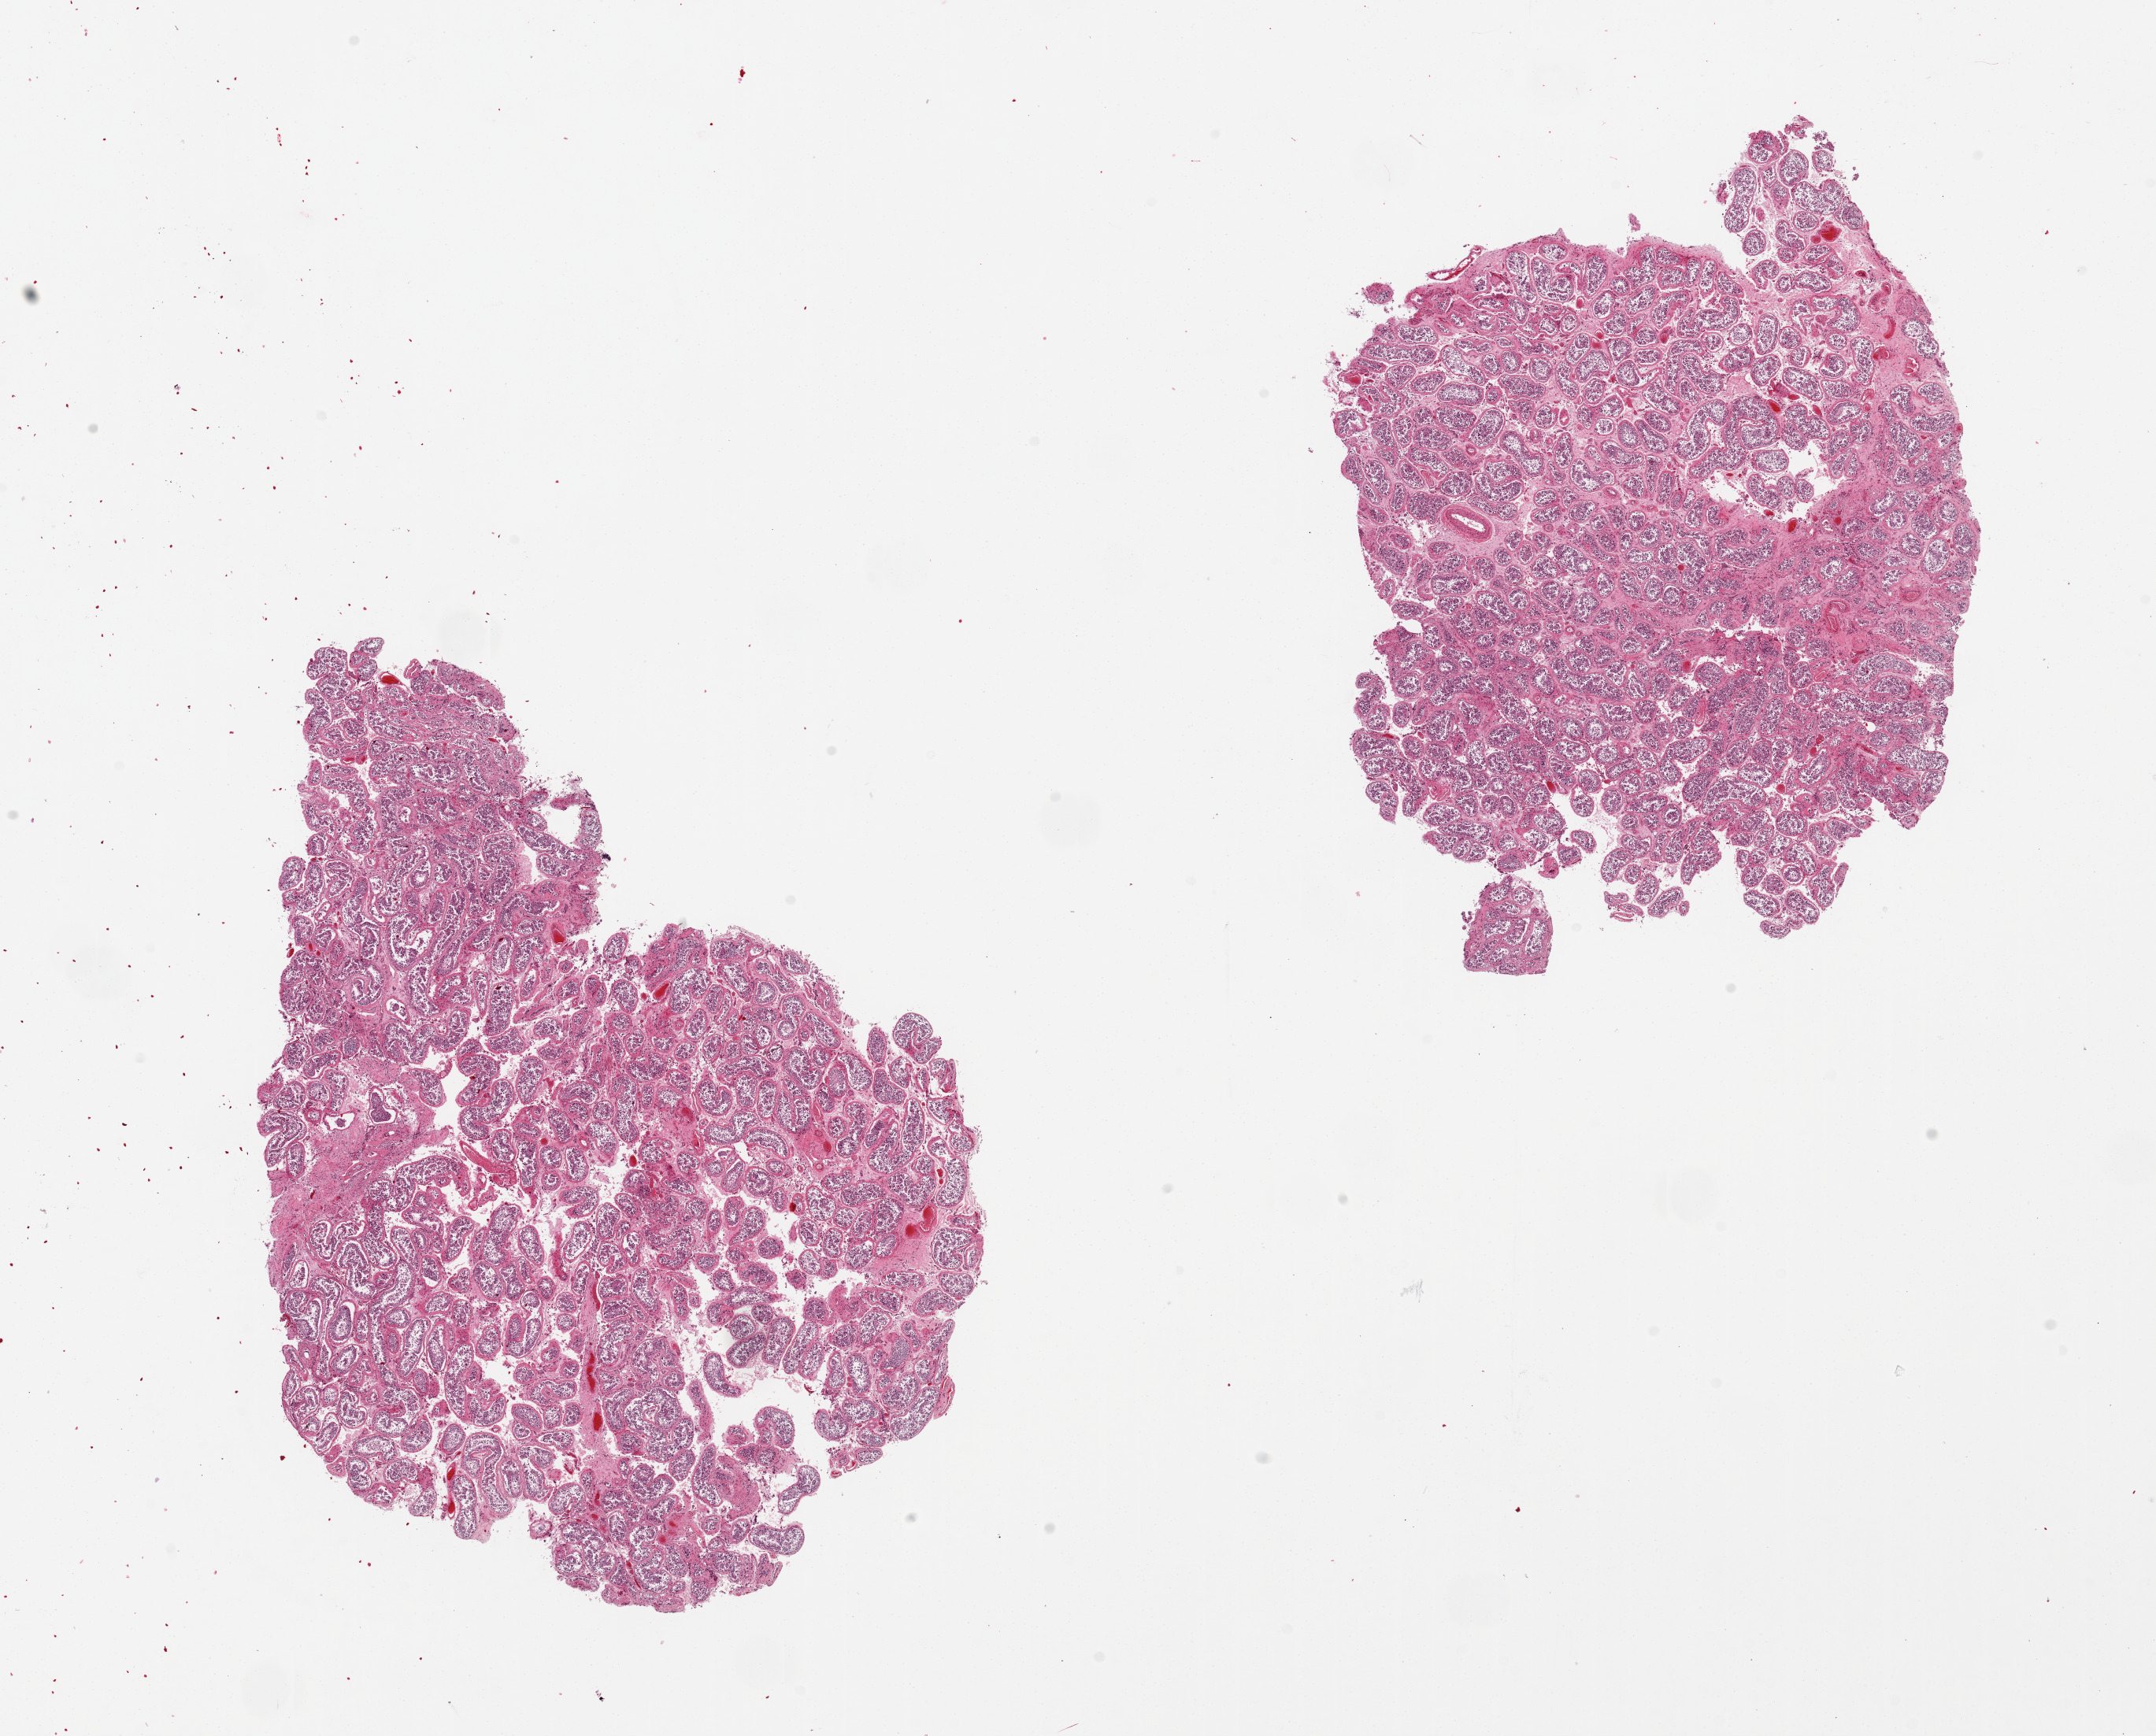
Digitized haematoxylin and eosin-stained section — a low-resolution overview of the entire scanned area, about 21.7 x 17.4 mm (acquisition: 20x scan), PAXgene-fixed paraffin-embedded (PFPE) section, target tissue: testis, donor tissue sample. Donor sex: male.
Pathologist's review note for this sample: 2 pieces, spermatogenesis present but cells badly autolyzed.